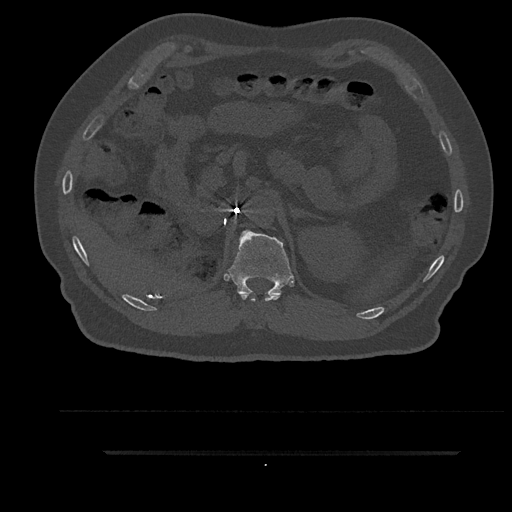
CT including the spine, one axial slice; position 262 of 797 along the scan axis; reconstruction kernel Br40s/3; bone window (W 1800 / L 400 HU); 512 × 512 image matrix, field of view 432 × 432 mm. Patient: male, 63 years. Case-level facts recorded for this patient, not image findings: primary cancer: renal.
Structures marked on this image (semi-automatic segmentation, software-assisted and operator-edited):
- T11 vertebra: bounding box (x1, y1, x2, y2) in pixels: (241, 294, 281, 302)
- T12 vertebra: (227, 229, 294, 295)